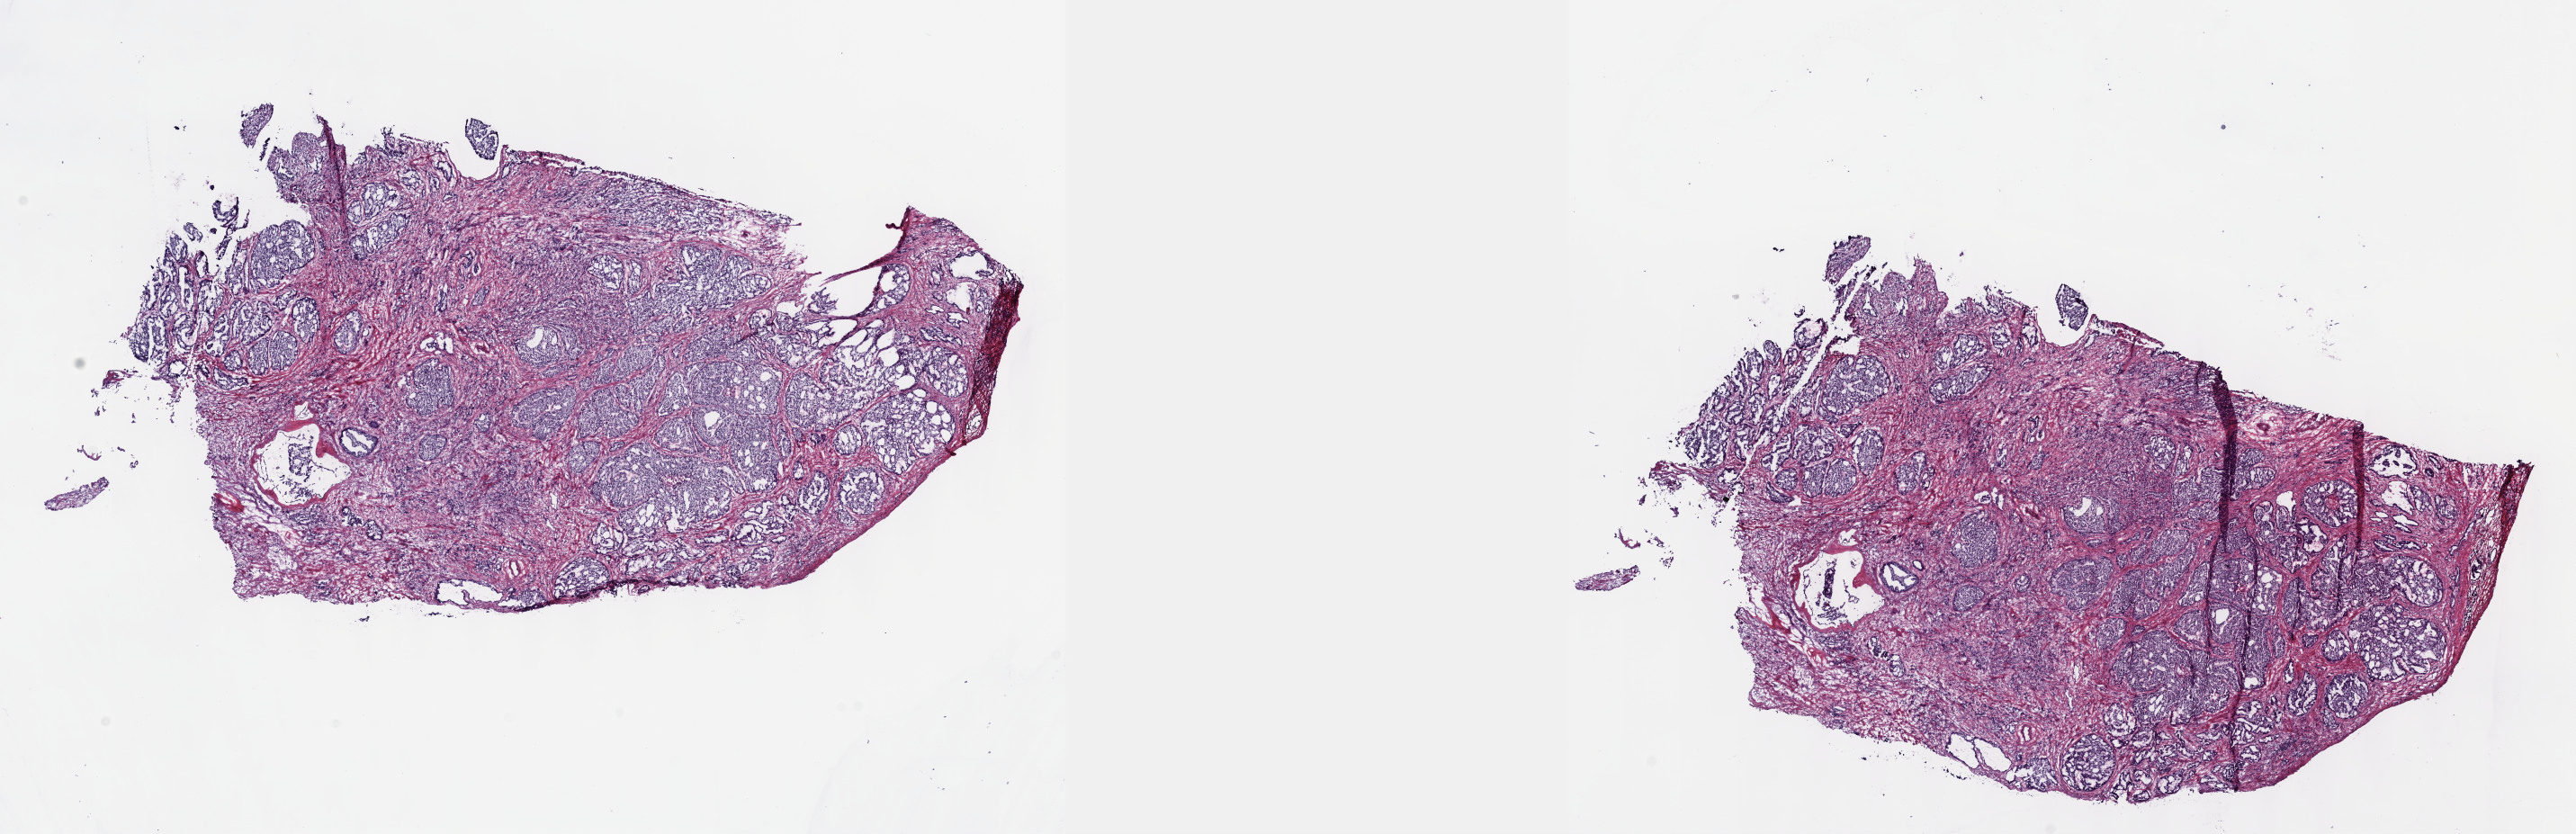
H&E-stained whole-slide image — a low-resolution overview of the entire scanned area, about 23.1 x 7.5 mm, frozen section from the top of the tissue portion, sample: primary tumour, prostate. Patient: male, age at initial diagnosis 67 years. Gleason score: 9 (5+4). Composition of this section per pathologist review: tumour cells 65%, tumour nuclei 70%, normal cells 5%, stromal cells 25%, necrosis 5%. Infiltration values recorded for this section: lymphocyte infiltration 5%, monocyte infiltration 0%, neutrophil infiltration 0%.
• lymph nodes positive (case pathology): 0 of 2 examined
• diagnosis: Mucinous adenocarcinoma
• laterality: right